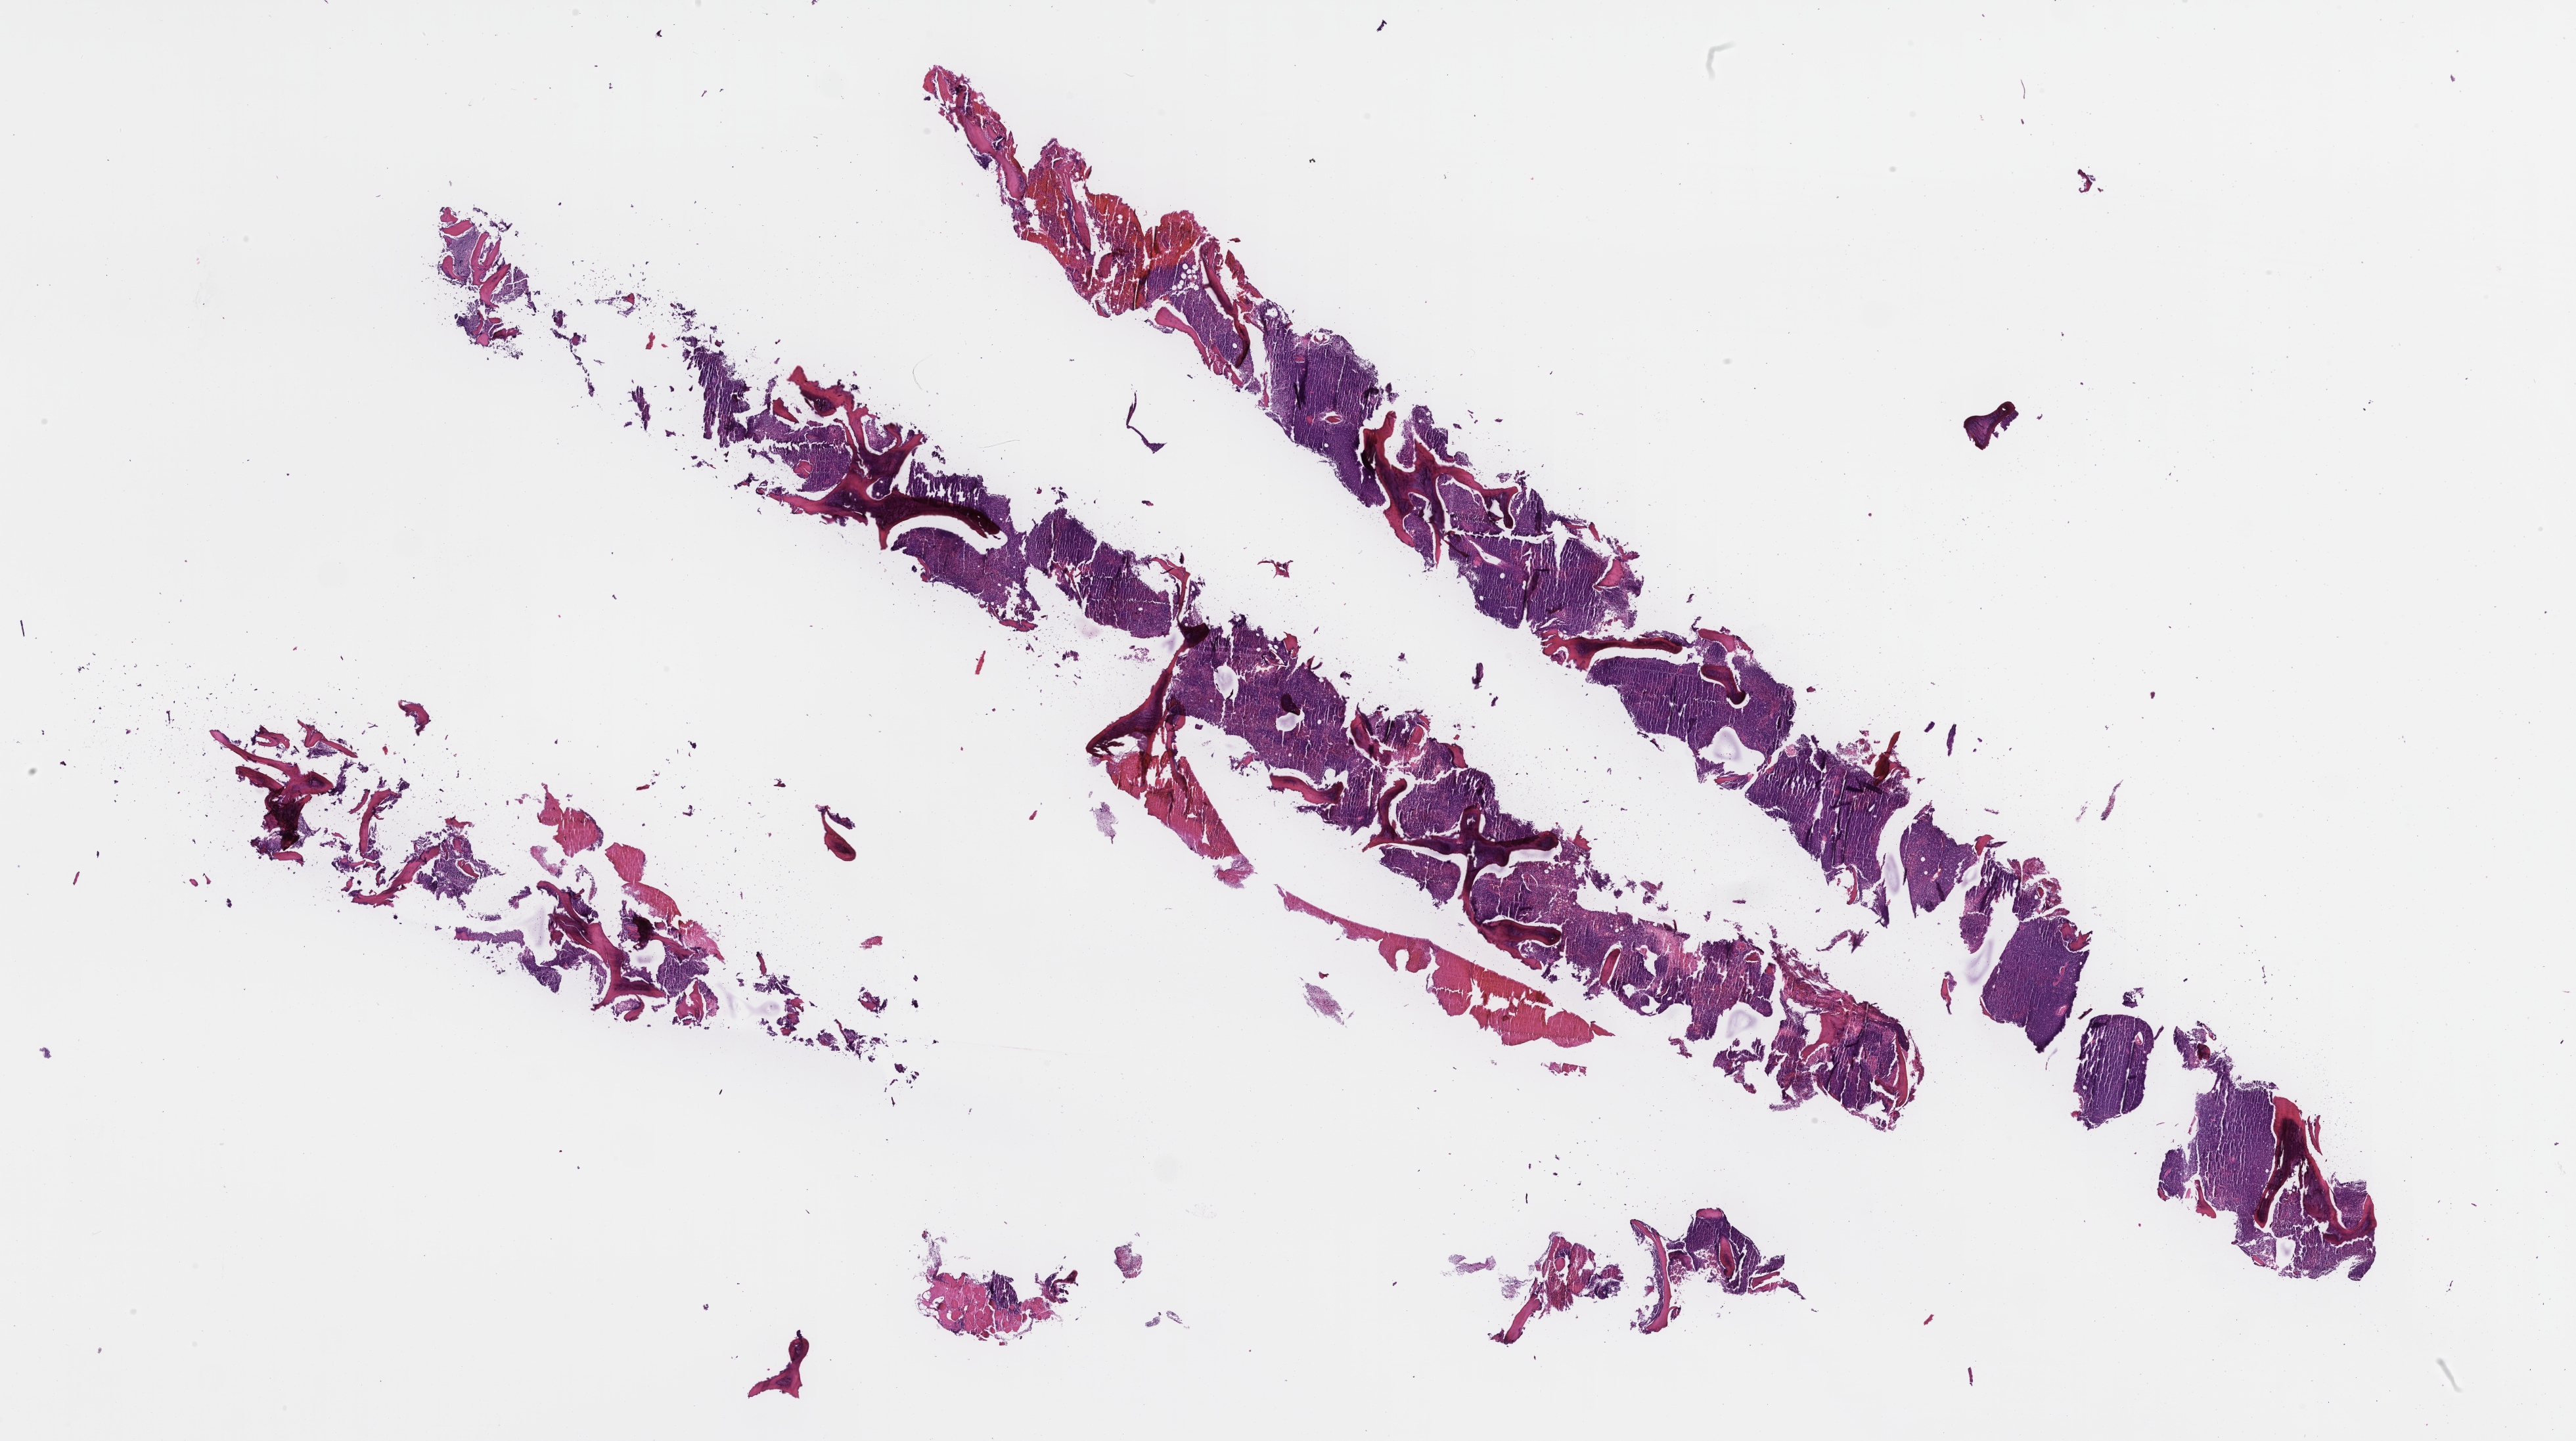
Digitized haematoxylin and eosin-stained section — a low-resolution overview of the entire scanned area, about 31.7 x 17.7 mm; formalin-fixed paraffin-embedded section; tissue site: bone marrow; specimen time point: archival tissue. Male patient.
* this section: primary tumor
* diagnosis: Plasma Cell Myeloma